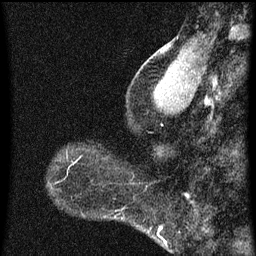
Breast MRI (dynamic contrast-enhanced), one sagittal slice; position 18 of 60 along the scan axis; dynamic contrast-enhanced series, image 2 of 3 at this slice position (ordered by acquisition); 1.5 T; TE 4.2 ms, TR 8 ms; 256 × 256 image matrix, field of view 180 × 180 mm. Female patient, age 44 years.
Structures marked on this image (semi-automatically segmented with operator editing):
- analysis volume of interest (the breast-tissue region the enhancement analysis was run in; not a lesion): bounding box <55,150,95,169> (left, top, right, bottom; pixels)
- tumour enhancement mask (voxels above the 70 % enhancement threshold inside the analysis volume of interest): <69,156,82,169>